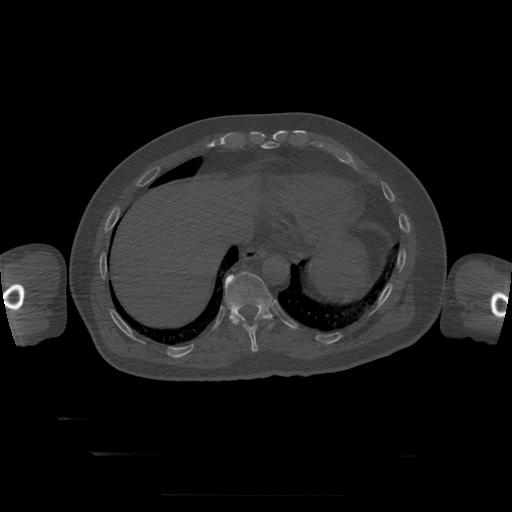
CT including the spine, one axial slice; position 111 of 397 along the scan axis; reconstruction kernel STANDARD; 120 kVp; bone window (W 1800 / L 400 HU); 1.25 mm slice thickness; 512 × 512 image matrix, field of view 510 × 510 mm. Patient age 73 years. From the clinical record (not read from this slice): primary cancer: prostate.
Outlined on this slice (semi-automatic segmentation, software-assisted and operator-edited):
- T10 vertebra: bounding box <230,318,269,352> (left, top, right, bottom; pixels)
- T11 vertebra: <225,272,273,329>